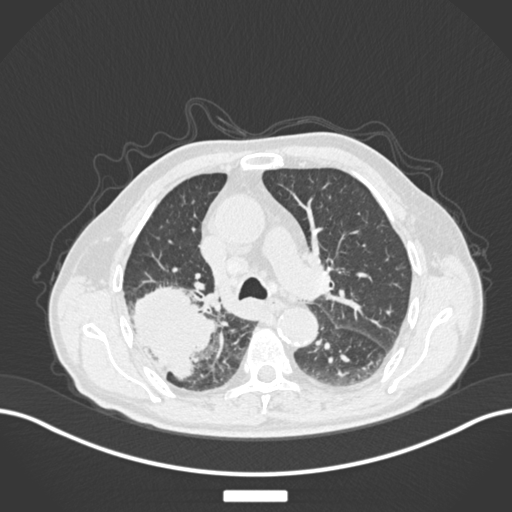
Chest CT, one axial slice; slice 117 of 201 in the series (ordered by position); reconstruction kernel B30f; 120 kVp; lung window (W 1500 / L -600 HU); 1 mm slice thickness; 512 × 512 image matrix. Patient: male, 72 years. From the clinical record (not read from this slice): clinical TNM (as recorded): T3 N2 M0.
Outlined on this slice (bounding box drawn by a radiologist):
- lung tumour (recorded histology: adenocarcinoma): bounding box [x1, y1, x2, y2] px = [131, 279, 217, 380]